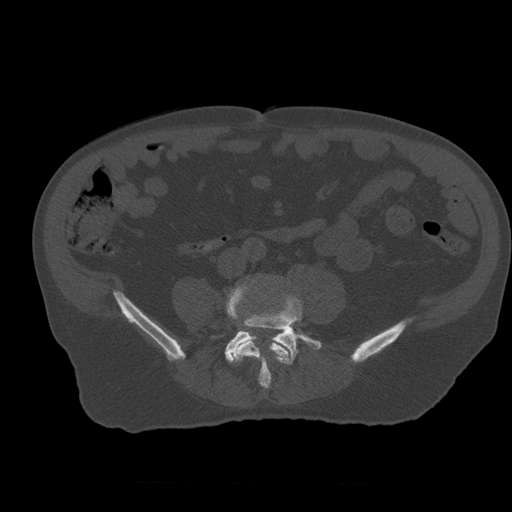
CT including the spine, one axial slice; position 152 of 399 along the scan axis; 120 kVp; bone window (W 1800 / L 400 HU); 1.25 mm slice thickness; 512 × 512 image matrix, field of view 407 × 407 mm. Patient age 73 years. Case-level facts recorded for this patient, not image findings: primary cancer: prostate; vertebrae with lytic lesions (as recorded): L2.
Outlined on this slice (semi-automatic segmentation, software-assisted and operator-edited):
- L4 vertebra: bounding box [x1, y1, x2, y2] px = [226, 281, 289, 389]
- L5 vertebra: [225, 300, 322, 381]